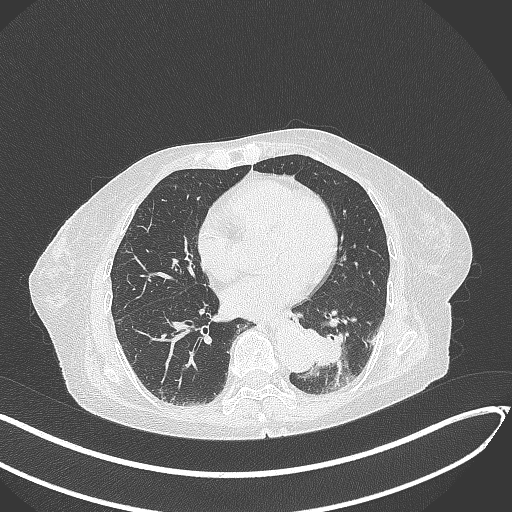
Chest CT, one axial slice. Position 99 of 324 along the scan axis. Lung window (W 1500 / L -600 HU). 1 mm slice thickness. 512 × 512 image matrix. Patient: female, 82 years. Case-level facts recorded for this patient, not image findings: clinical TNM (as recorded): T1b N0 M1.
Annotated regions visible in this slice (rectangle marked by the reading radiologist):
- lung tumour (recorded histology: adenocarcinoma): box from (x=300, y=325) to (x=357, y=369) px